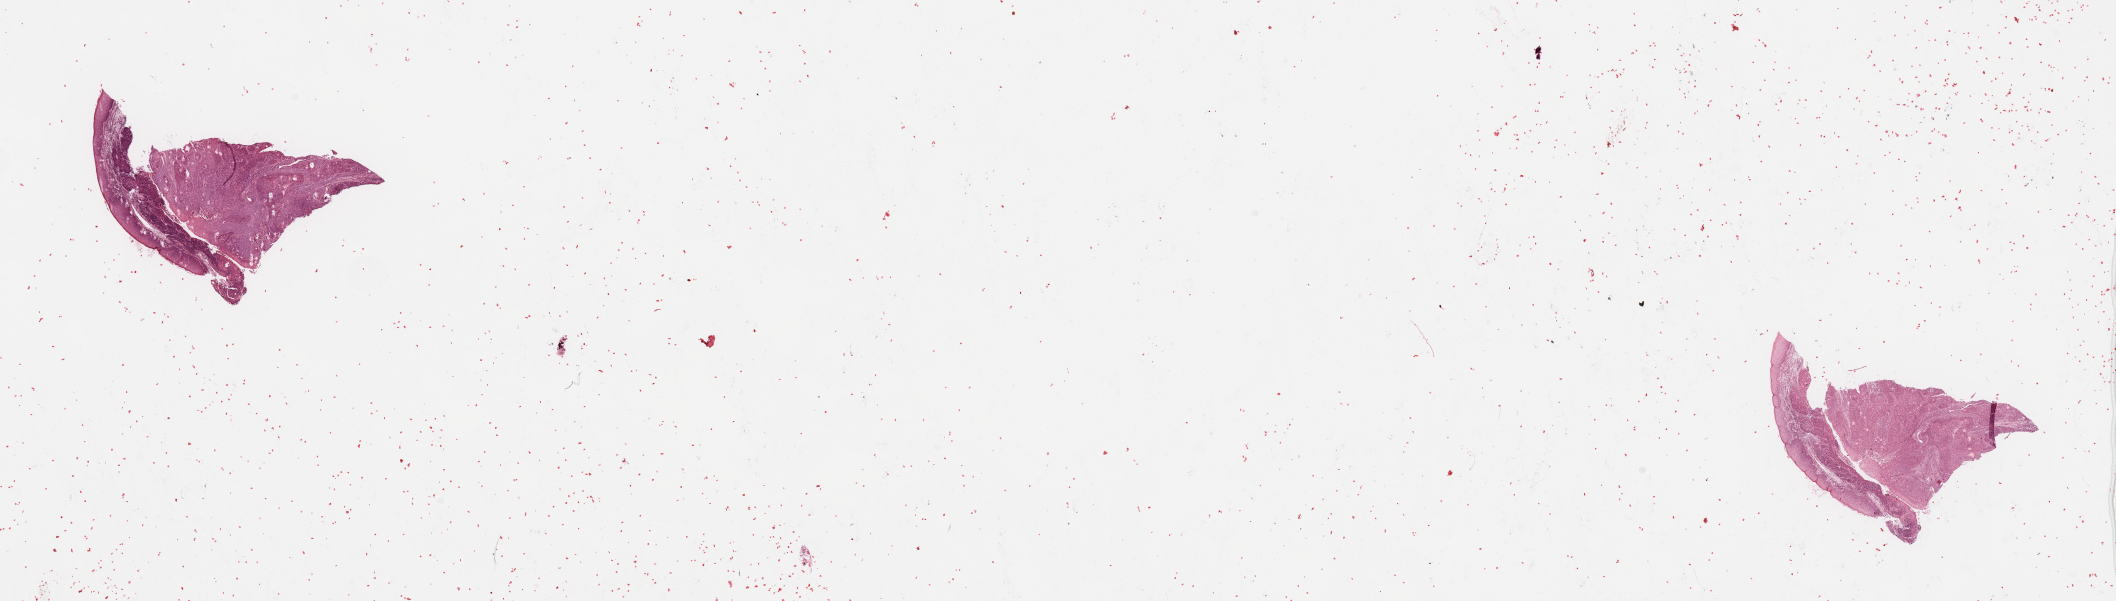
Whole-slide histology image, Hematoxylin and eosin (H&E) stained, whole scanned area (about 33.5 x 9.5 mm, slide scanned at 20x) shown as a low-resolution overview; tumour tissue sample, sampled site: larynx. Male, 67 y/o. Histologic grade: G2 (moderately differentiated). Pathologist review of this section (percent, as recorded): tumour nuclei 80%, necrosis 2%.
Primary tumour site (as recorded): larynx. AJCC pathologic stage: IVA. Histologic diagnosis: Squamous cell carcinoma, NOS (larynx, NOS).